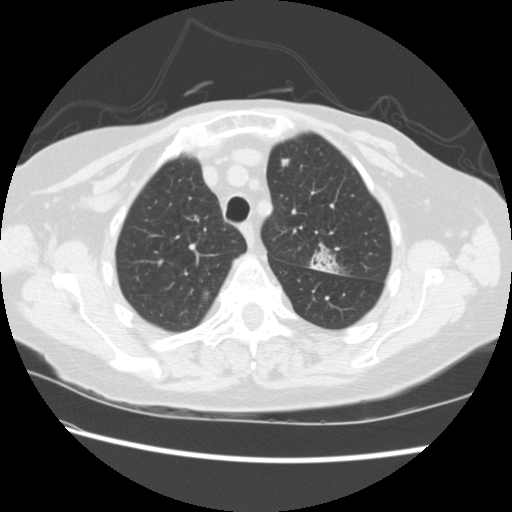
Low-dose screening chest CT, one axial slice. Slice 171 of 224 in the series (ordered by position). Lung window (W 1500 / L -600 HU). 2.5 mm slice thickness. 512 × 512 image matrix.
Structures marked on this image (expert manual segmentation):
- lesion 1 (tumor, upper lobe of left lung): bounding box (x1, y1, x2, y2) in pixels: (310, 245, 338, 273)